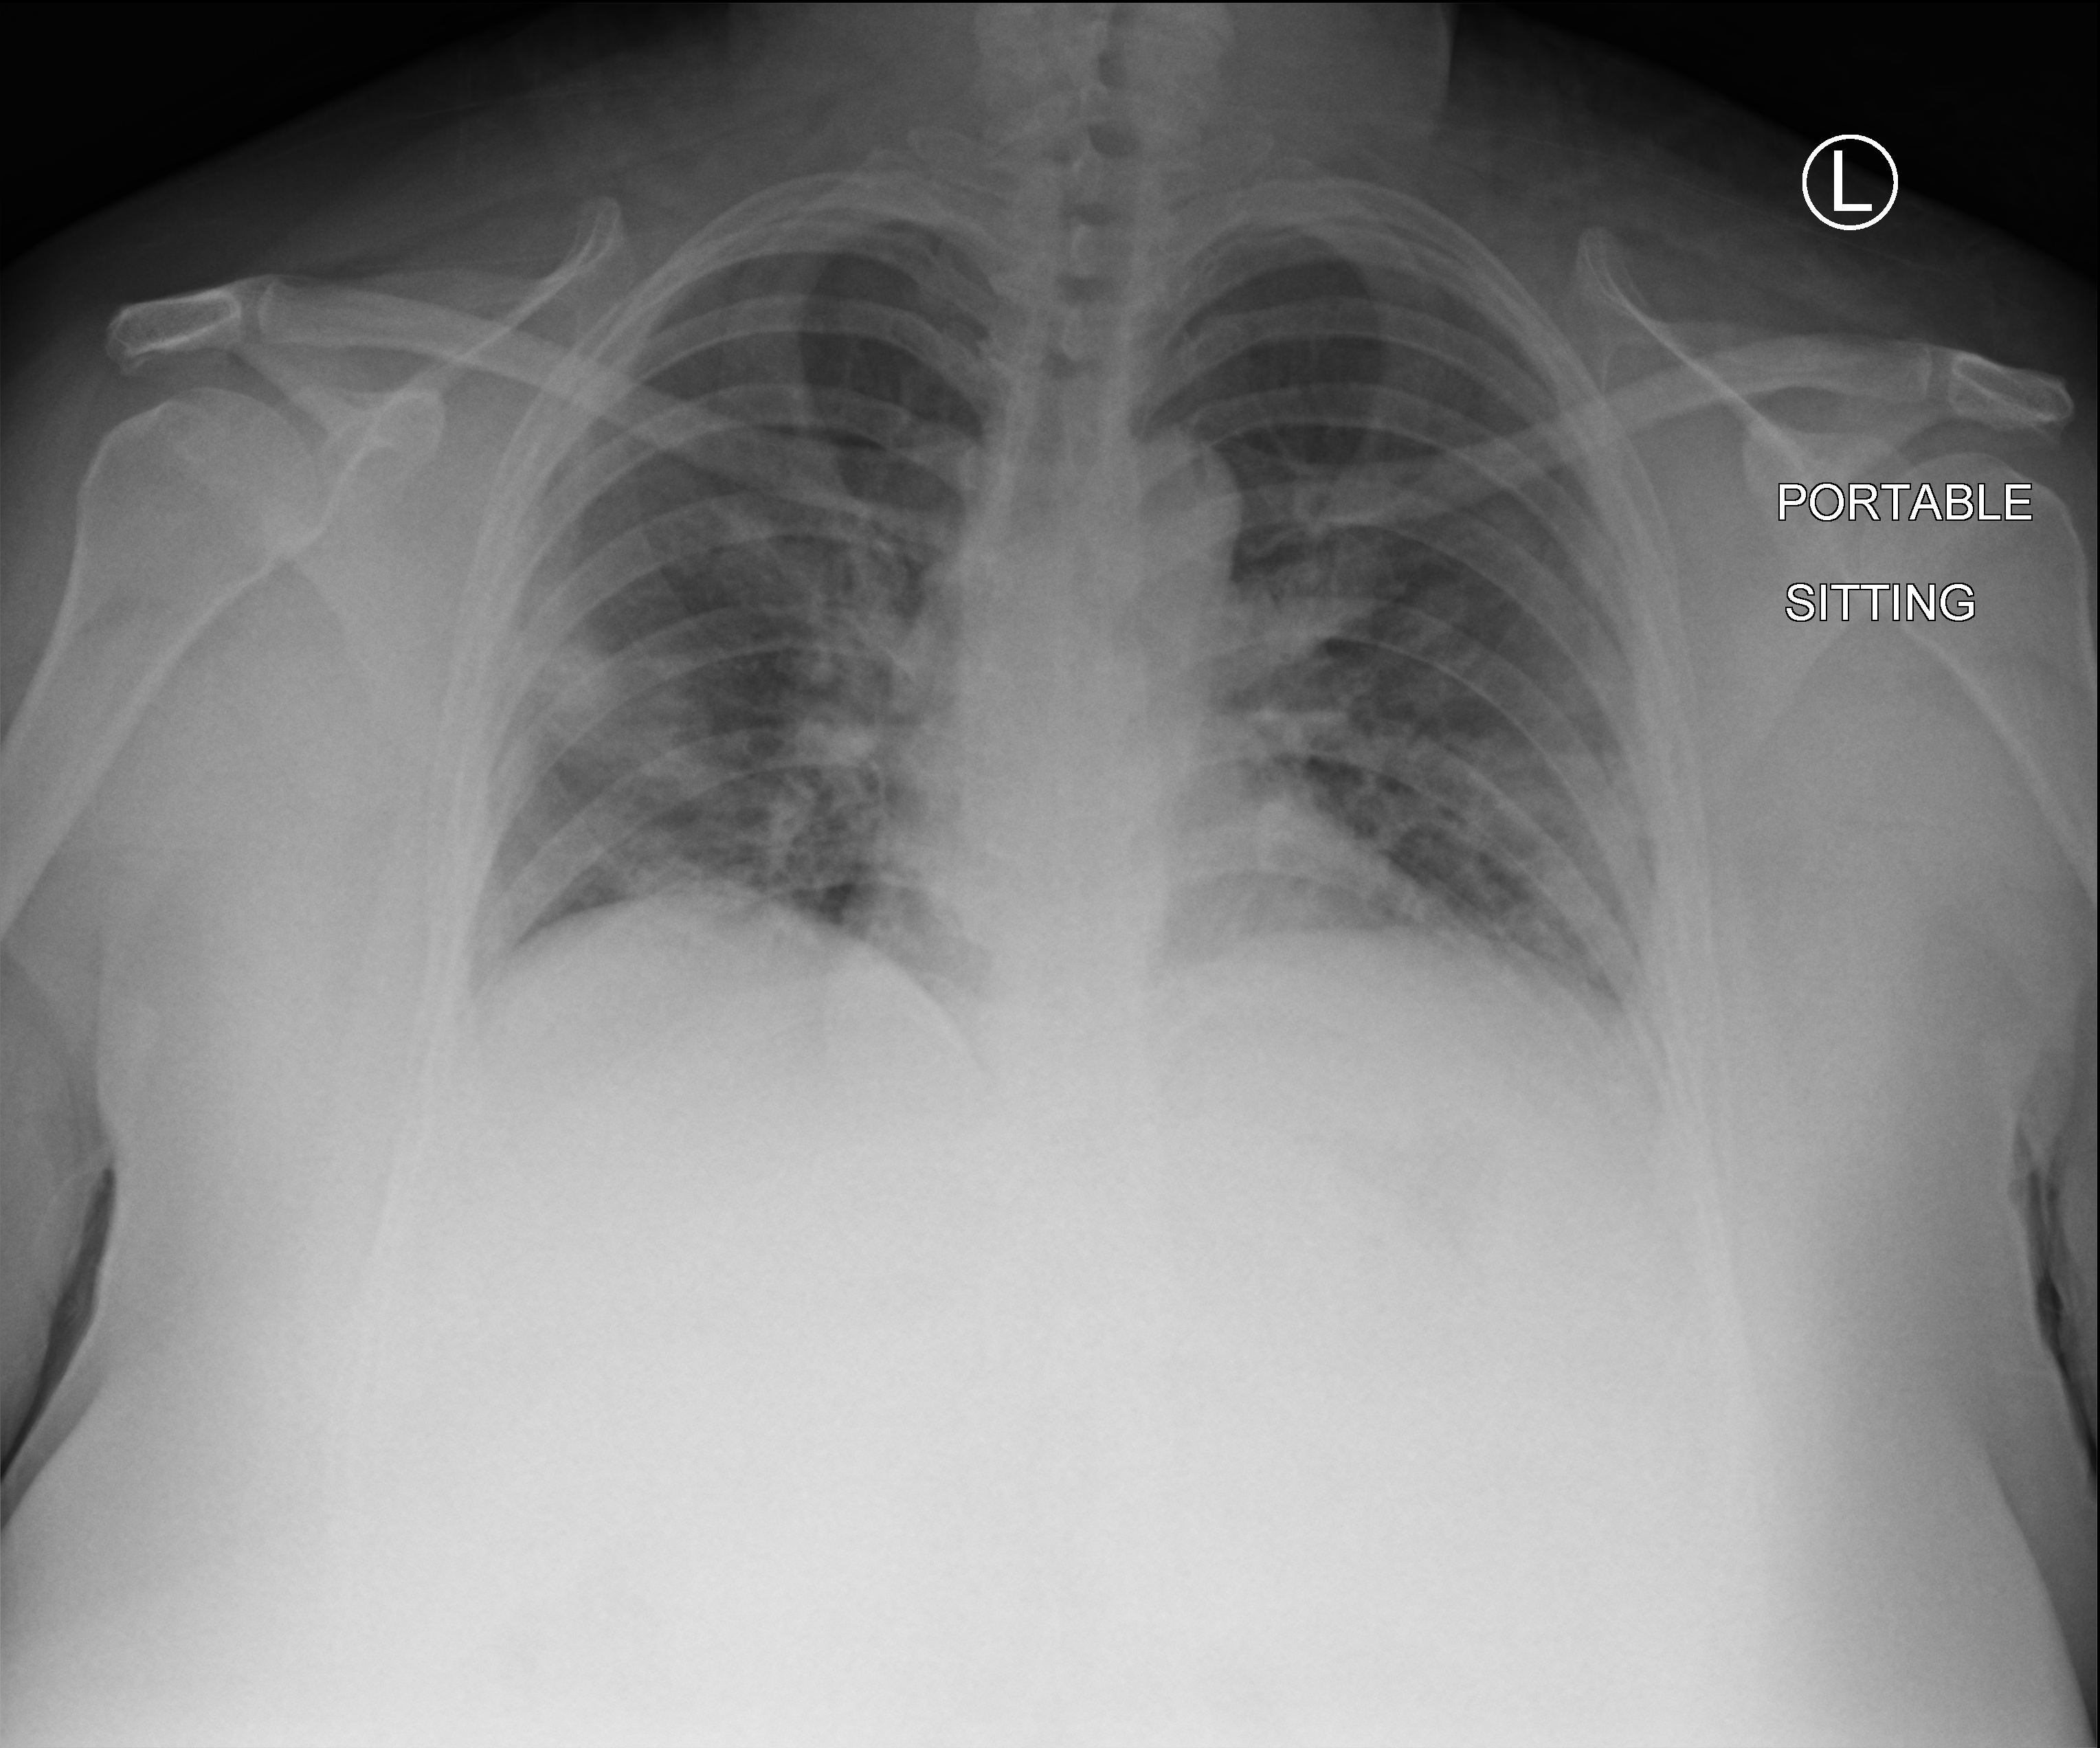
Chest X-ray (portable), anteroposterior (AP) projection. Female patient hospitalised with COVID-19, age 18–59 years.
From the hospital-stay record, not from the radiograph (when in the stay this image was taken is not recorded): admitted to intensive care during this hospital stay: no.